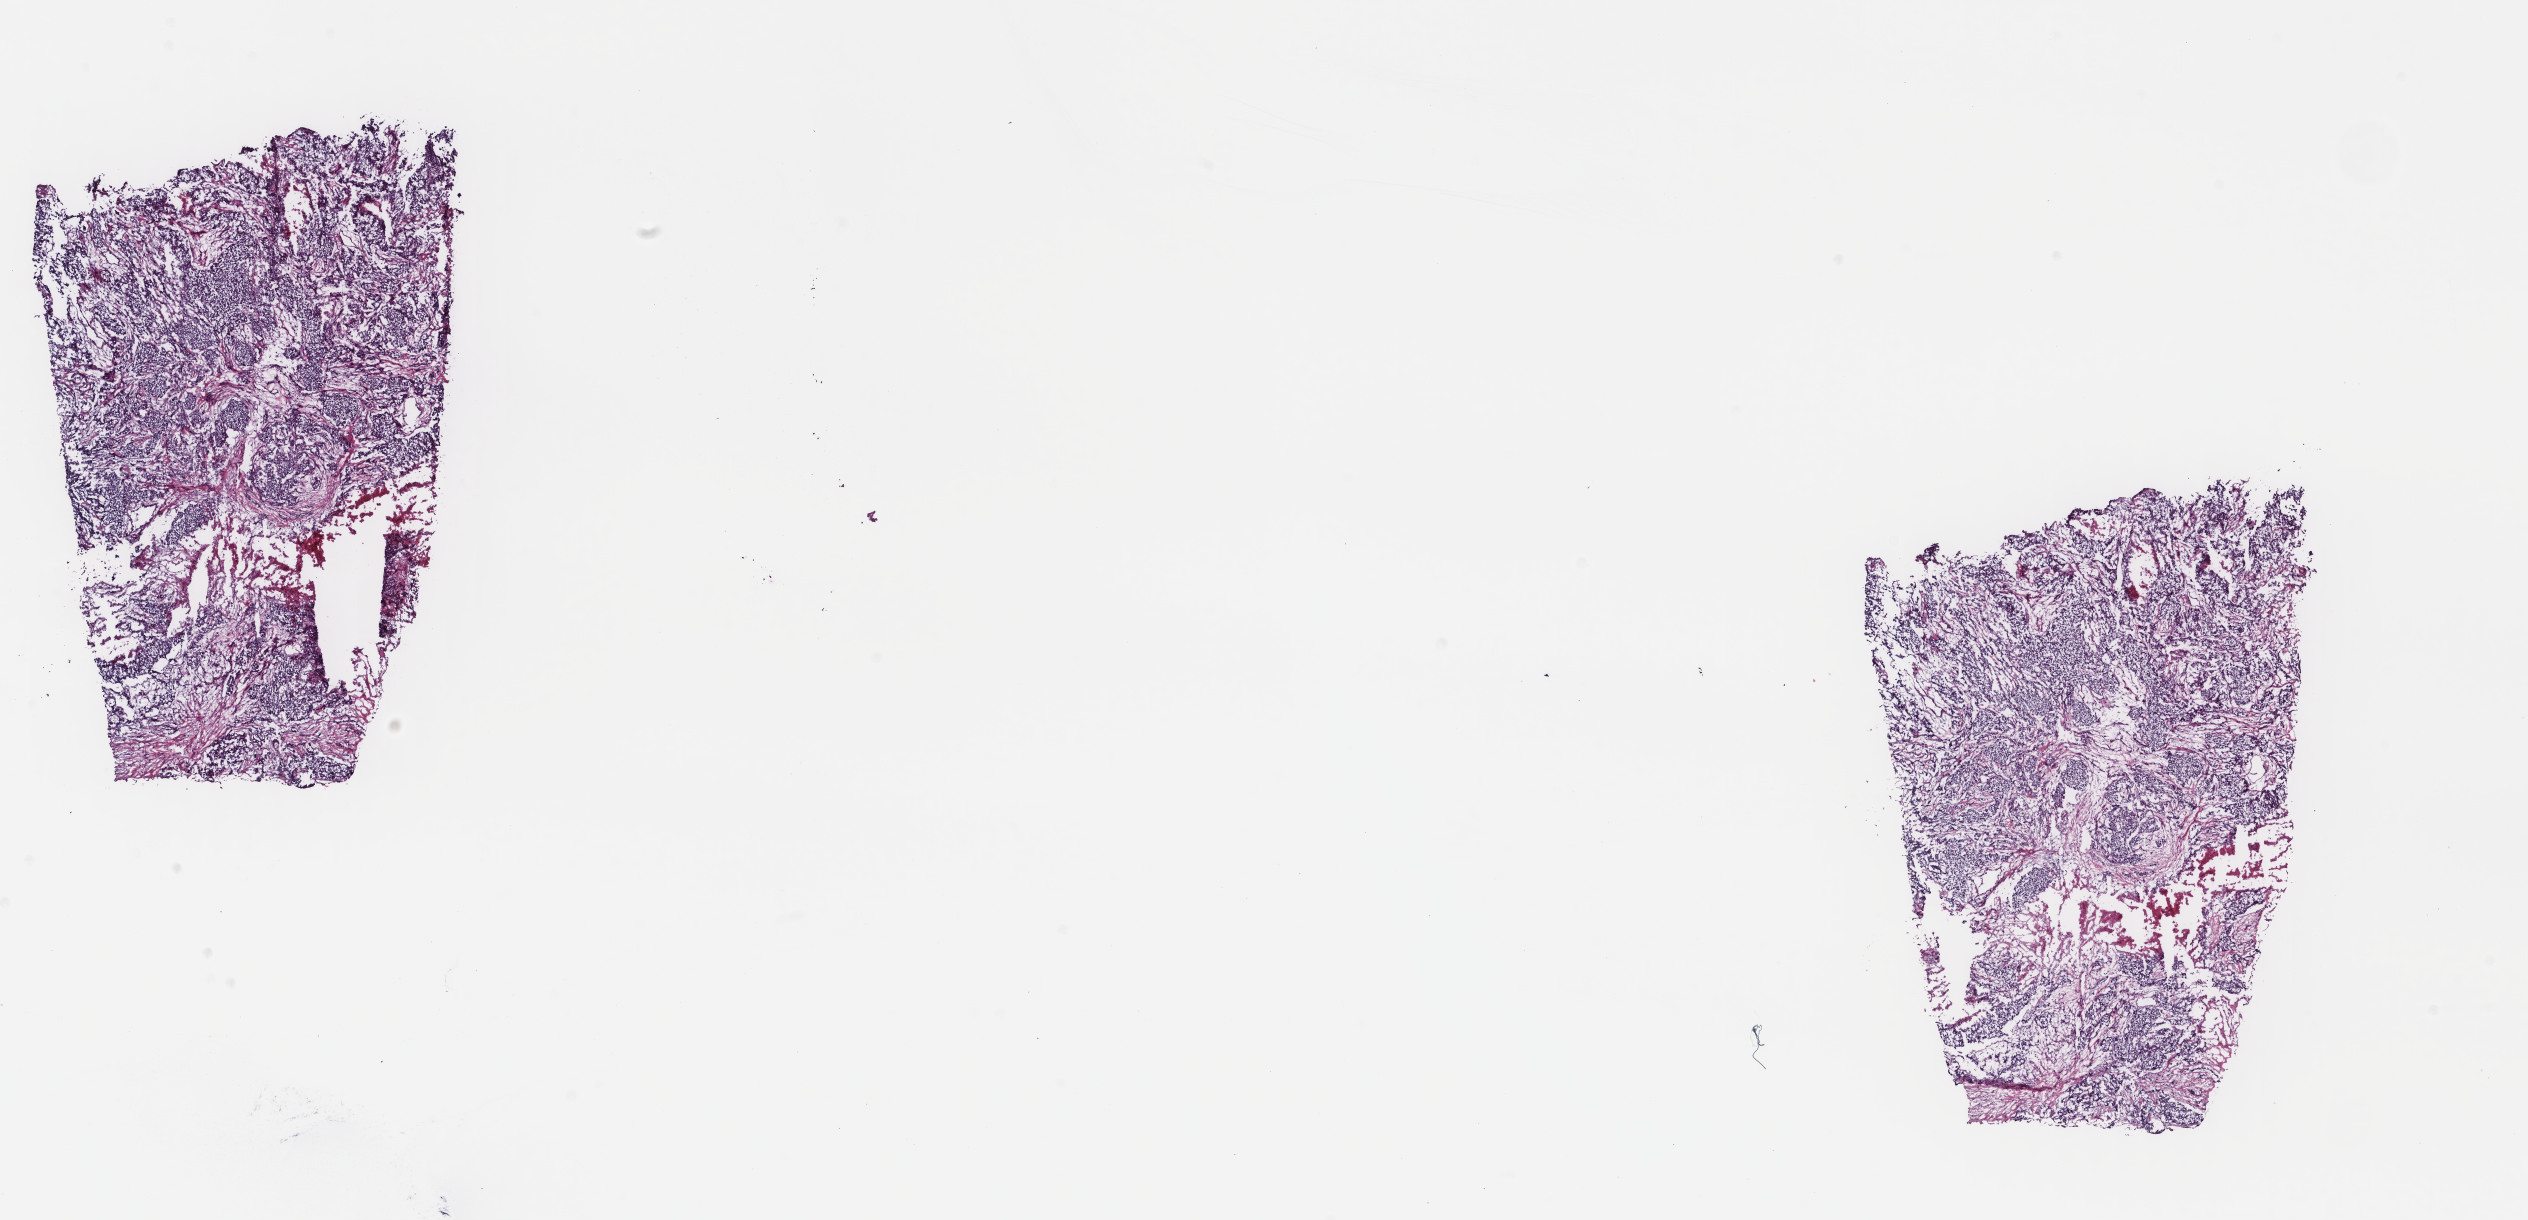
Hematoxylin and eosin (H&E) stained whole-slide image, whole scanned area (about 20.1 x 9.7 mm) shown as a low-resolution overview; frozen section from the top of the tissue portion; breast, primary tumour sample. Female, age 60 years at initial diagnosis. Slide review estimates, as recorded: tumour cells 90%, tumour nuclei 95%, normal cells 0%, stromal cells 0%, necrosis 10%. Infiltration values recorded for this section: lymphocyte infiltration 0%, monocyte infiltration 0%, neutrophil infiltration 0%.
* diagnosis: Infiltrating duct carcinoma, NOS